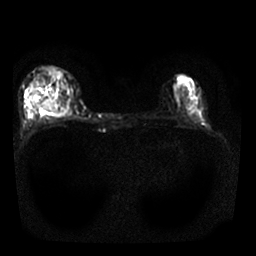
Breast MRI, one axial slice; slice 11 of 25 in the series (ordered by position); diffusion-weighted series; image 2 of 4 stored at this slice position (different b-values; order by instance number); 1.5 T; 4 mm slice thickness; 256 × 256 image matrix, field of view 310 × 310 mm. Female patient.
Structures marked on this image (outlined manually by an expert reader):
- tumour on diffusion-weighted imaging: bounding box <43,101,62,114> (left, top, right, bottom; pixels)